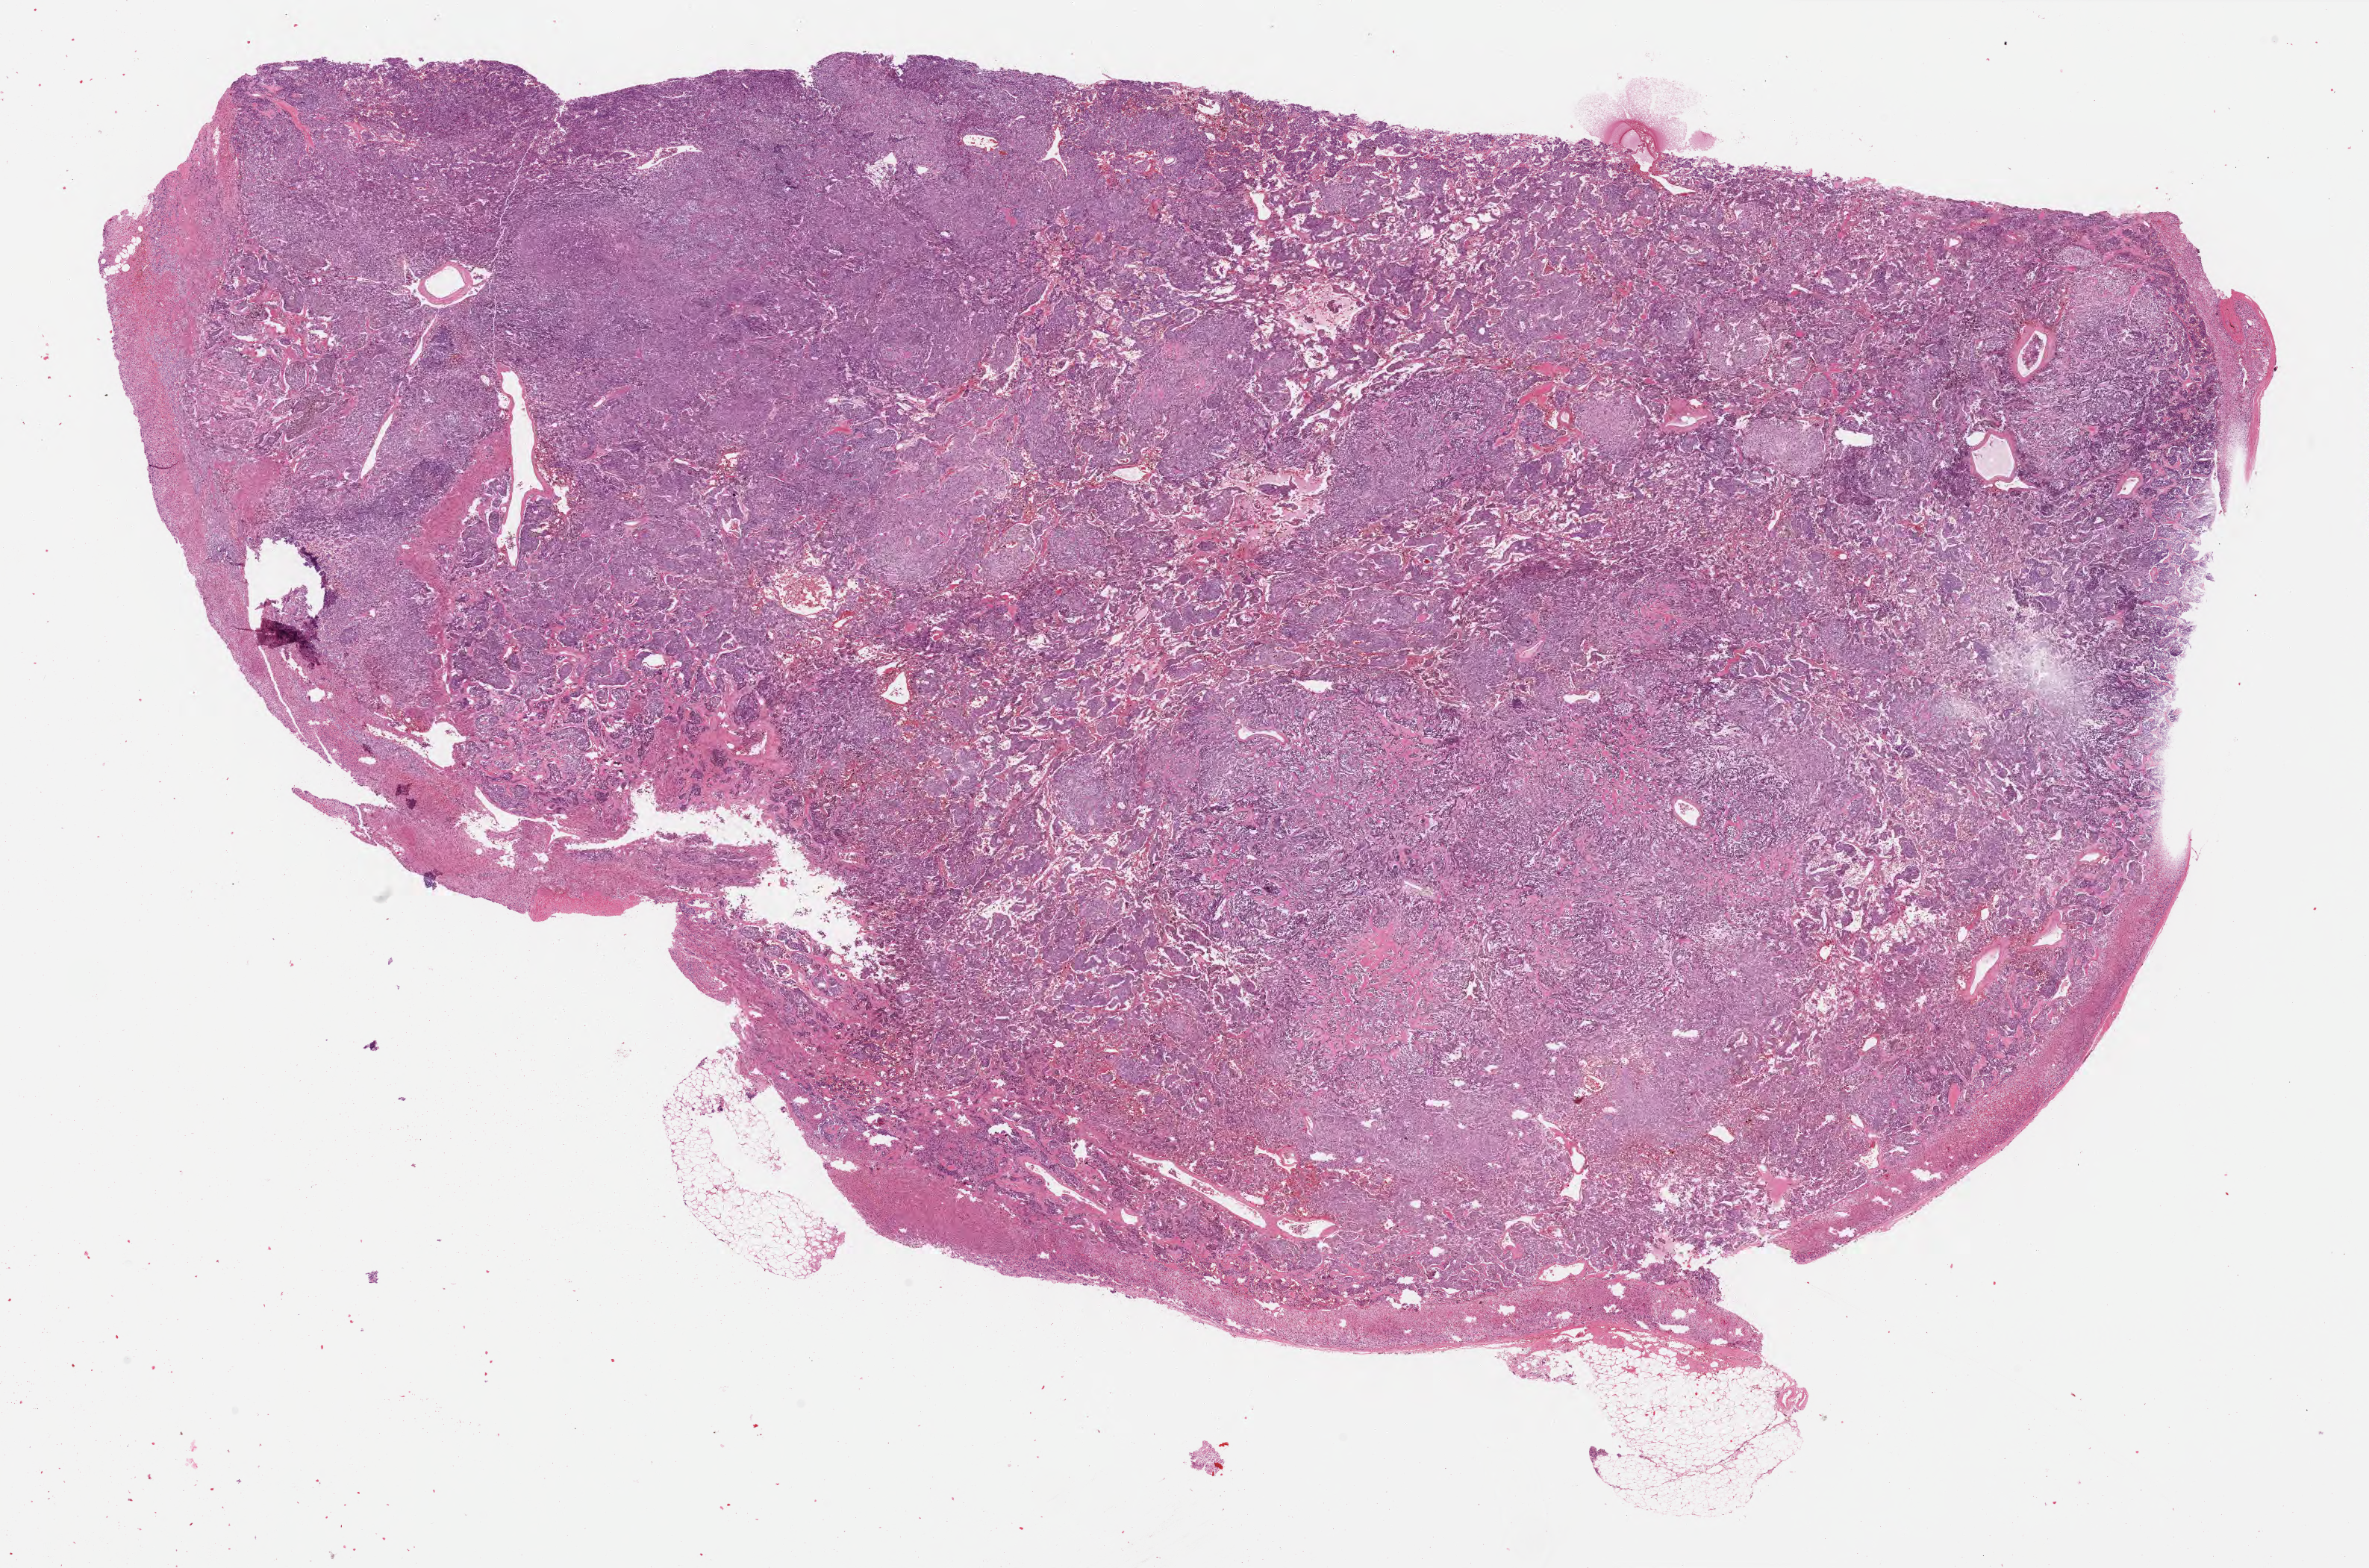
Whole-slide histology image, H&E, whole scanned area (about 25.0 x 16.5 mm, acquisition: 40x scan) shown as a low-resolution overview; formalin-fixed paraffin-embedded (FFPE) diagnostic section; sample: primary tumour, adrenal gland. Patient: female, age at initial diagnosis 50 years.
Diagnosis: Pheochromocytoma, NOS.